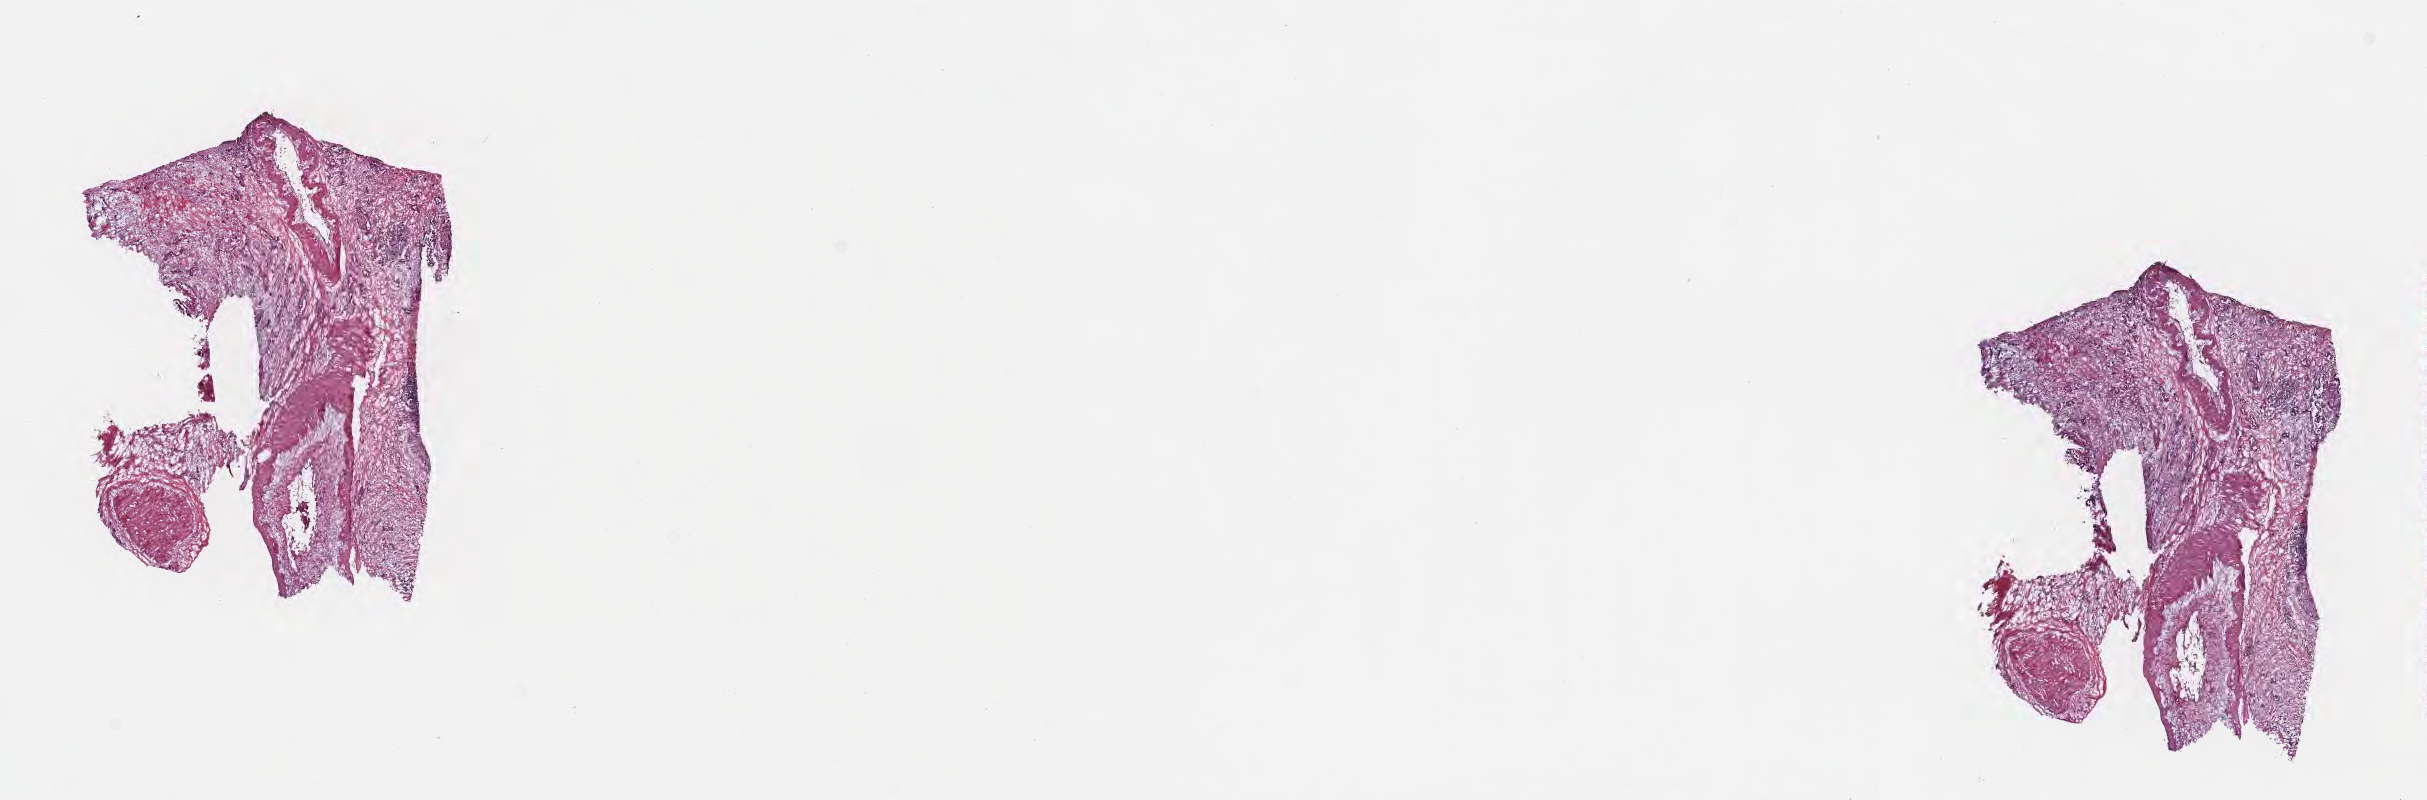
Whole-slide image, H&E stain, whole scanned area (about 19.6 x 6.5 mm) shown as a low-resolution overview, frozen section, primary tumor, site: head of pancreas. Patient: male, age at initial diagnosis 69 years. Tumor grade: G2 (moderately differentiated). Pathologist review of this section (percent, as recorded): tumor cells 20%, tumor nuclei 20%, stromal cells 65%, necrosis 0%, normal cells 15%. Inflammatory infiltration, as recorded: lymphocyte infiltration 10%, monocyte infiltration 0%, neutrophil infiltration 2%.
• histologic diagnosis: Infiltrating duct carcinoma, NOS
• section: top of the tissue portion
• AJCC pathologic stage: Stage III